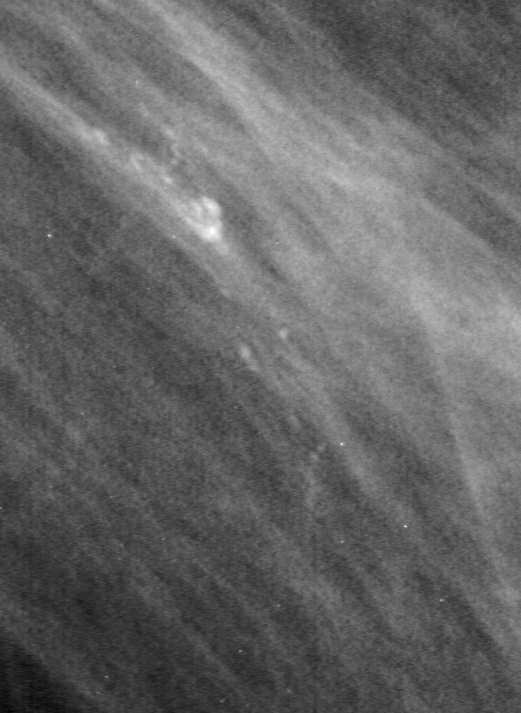
Cropped region of a digitized screen-film mammogram centred on a radiologist-marked abnormality, right breast, MLO view, BI-RADS breast density category 1 (scale 1–4).
Marked abnormality: calcifications, morphology pleomorphic / fine linear branching, distribution linear; BI-RADS assessment category 5; pathology (as recorded): malignant.